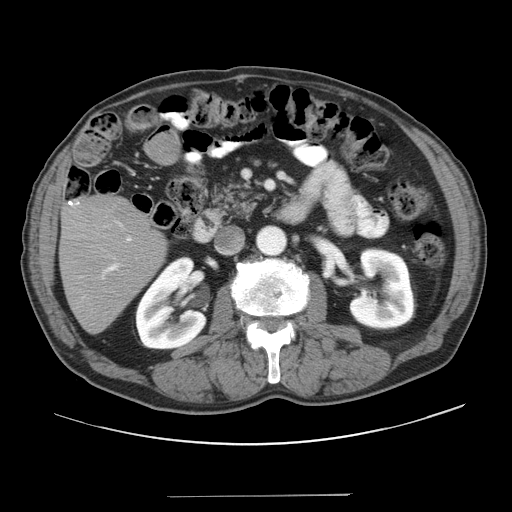
Contrast-enhanced abdominal CT, one axial slice; slice 12 of 41 in the series (ordered by position); reconstruction kernel STANDARD; intravenous contrast given; soft-tissue window (W 400 / L 40 HU); 5 mm slice thickness; 512 × 512 image matrix, field of view 420 × 420 mm. Male patient, age 75 years. Case-level facts recorded for this patient, not image findings: diagnosis: colorectal cancer liver metastases, imaged before liver resection; multiple liver metastases: no; largest metastasis: 5.2 cm.
Annotated regions visible in this slice (outlined manually by an expert reader):
- liver: box from (x=60, y=195) to (x=167, y=333) px
- planned liver remnant (the part of the liver to remain after resection): (x=60, y=195)–(x=167, y=333)
- portal vein (with intrahepatic branches): (x=101, y=221)–(x=132, y=279)